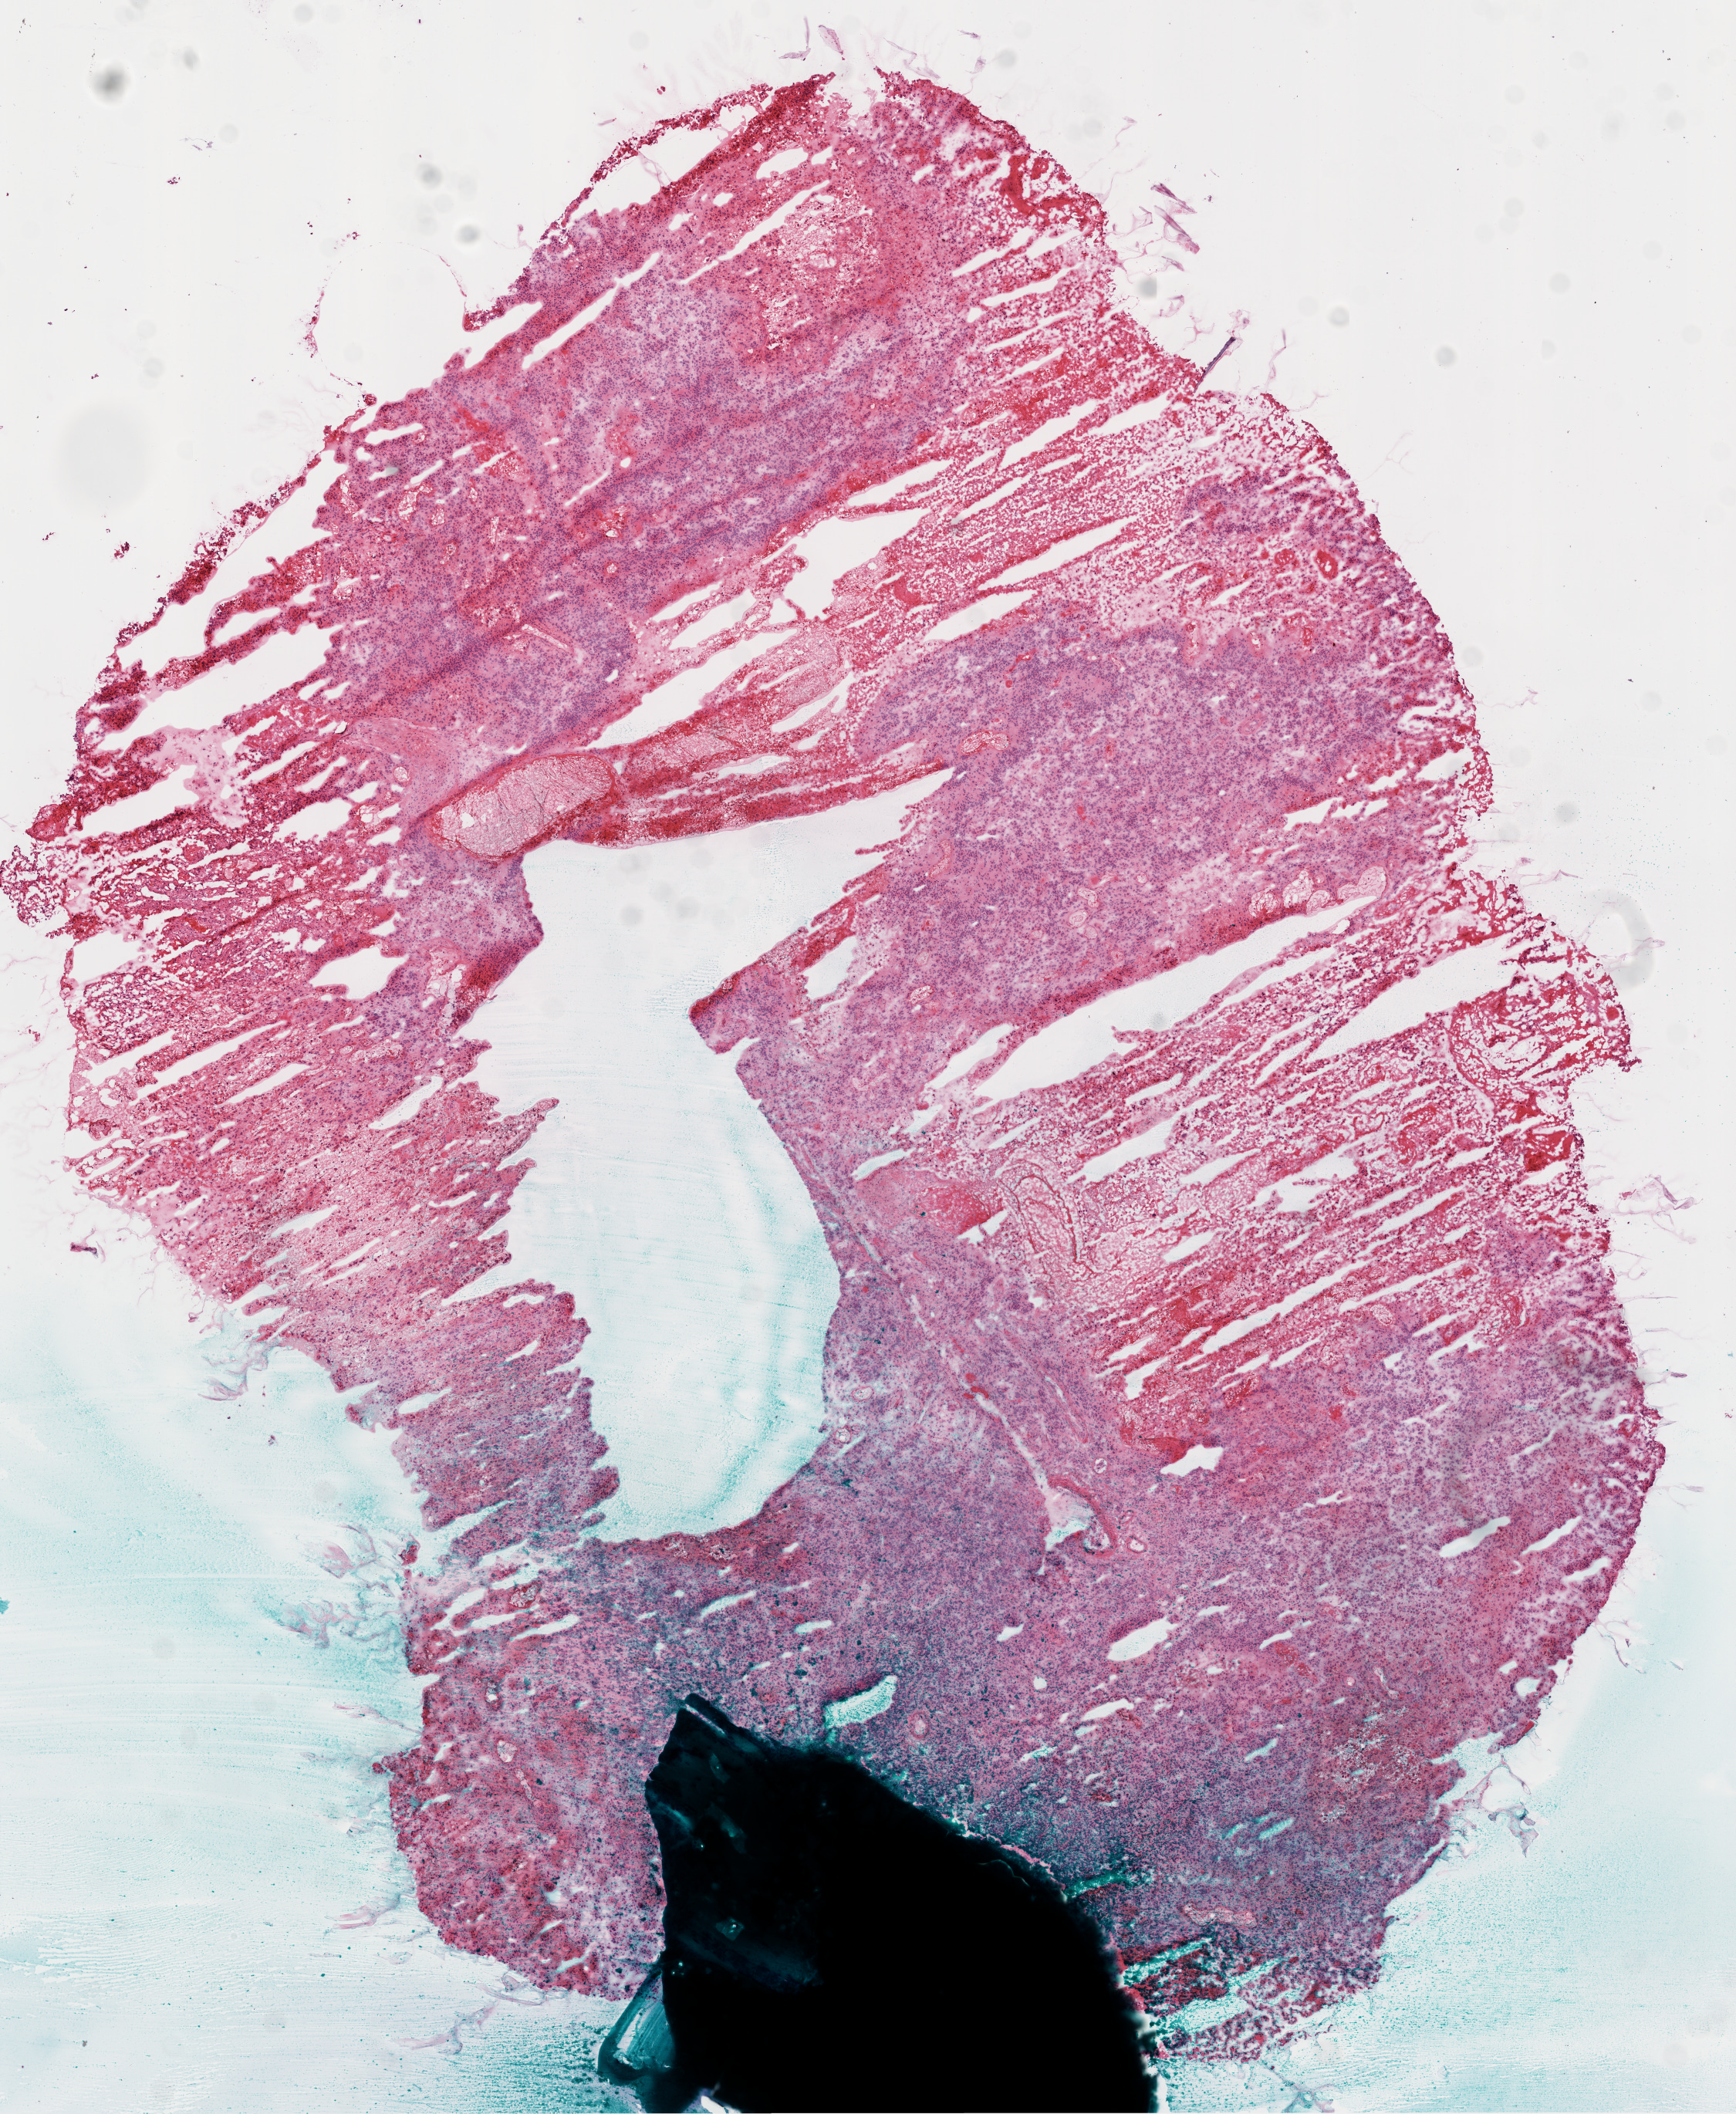
Hematoxylin and eosin (H&E) stained whole-slide image — whole scanned area (about 9.0 x 11.0 mm, from a 20x scan) shown as a low-resolution overview. Frozen section from the bottom of the tissue portion. Brain, primary tumour sample. Patient: female, age at initial diagnosis 36 years. Slide review estimates, as recorded: tumour cells 60%, tumour nuclei 100%, normal cells 0%, stromal cells 0%, necrosis 40%.
• diagnosis: Glioblastoma